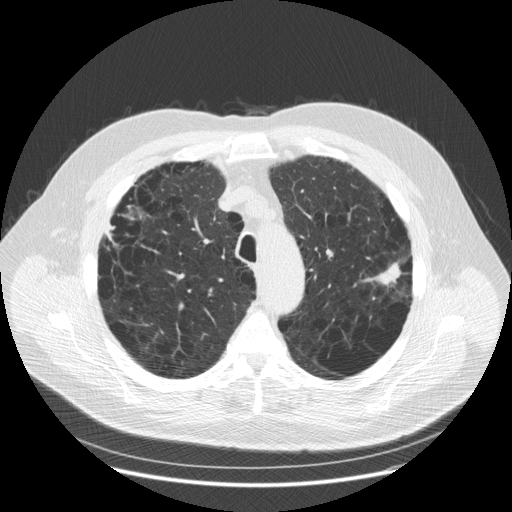
Low-dose screening chest CT, one axial slice. Position 135 of 179 along the scan axis. Reconstruction kernel STANDARD. Lung window (W 1500 / L -600 HU). 512 × 512 image matrix, field of view 404 × 404 mm.
Structures marked on this image (manually delineated by an expert):
- lesion 1 (tumor, upper lobe of left lung): bounding box (x1, y1, x2, y2) in pixels: (362, 262, 402, 287)